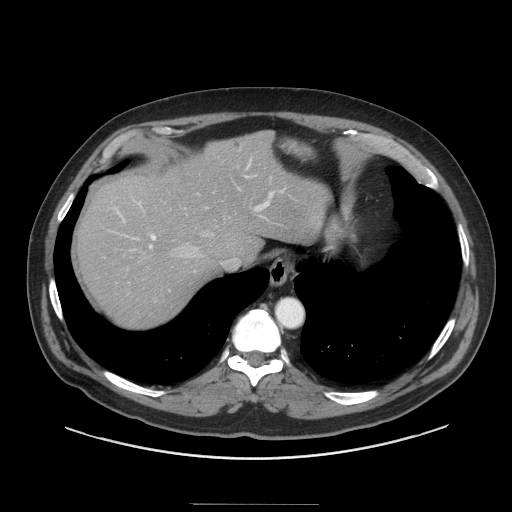
Contrast-enhanced abdominal CT (liver protocol), one axial slice; position 76 of 91 along the scan axis; reconstruction kernel STANDARD; soft-tissue window (W 400 / L 40 HU); 2.5 mm slice thickness; 512 × 512 image matrix, field of view 440 × 440 mm. Case-level facts recorded for this patient, not image findings: diagnosis: hepatocellular carcinoma (patient treated with transarterial chemoembolisation; whether this scan precedes or follows treatment is not stated here); TNM stage (as recorded): Stage-I; Child-Pugh class: A; tumour differentiation: well differentiated.
Structures marked on this image (semi-automatic segmentation, software-assisted and operator-edited):
- abdominal aorta: bounding box [x1, y1, x2, y2] px = [278, 299, 302, 326]
- liver parenchyma outside the tumour (the mass and vessels are separate outlines, so this box may not span the whole liver): [74, 130, 328, 324]
- liver vessels: [114, 159, 284, 257]